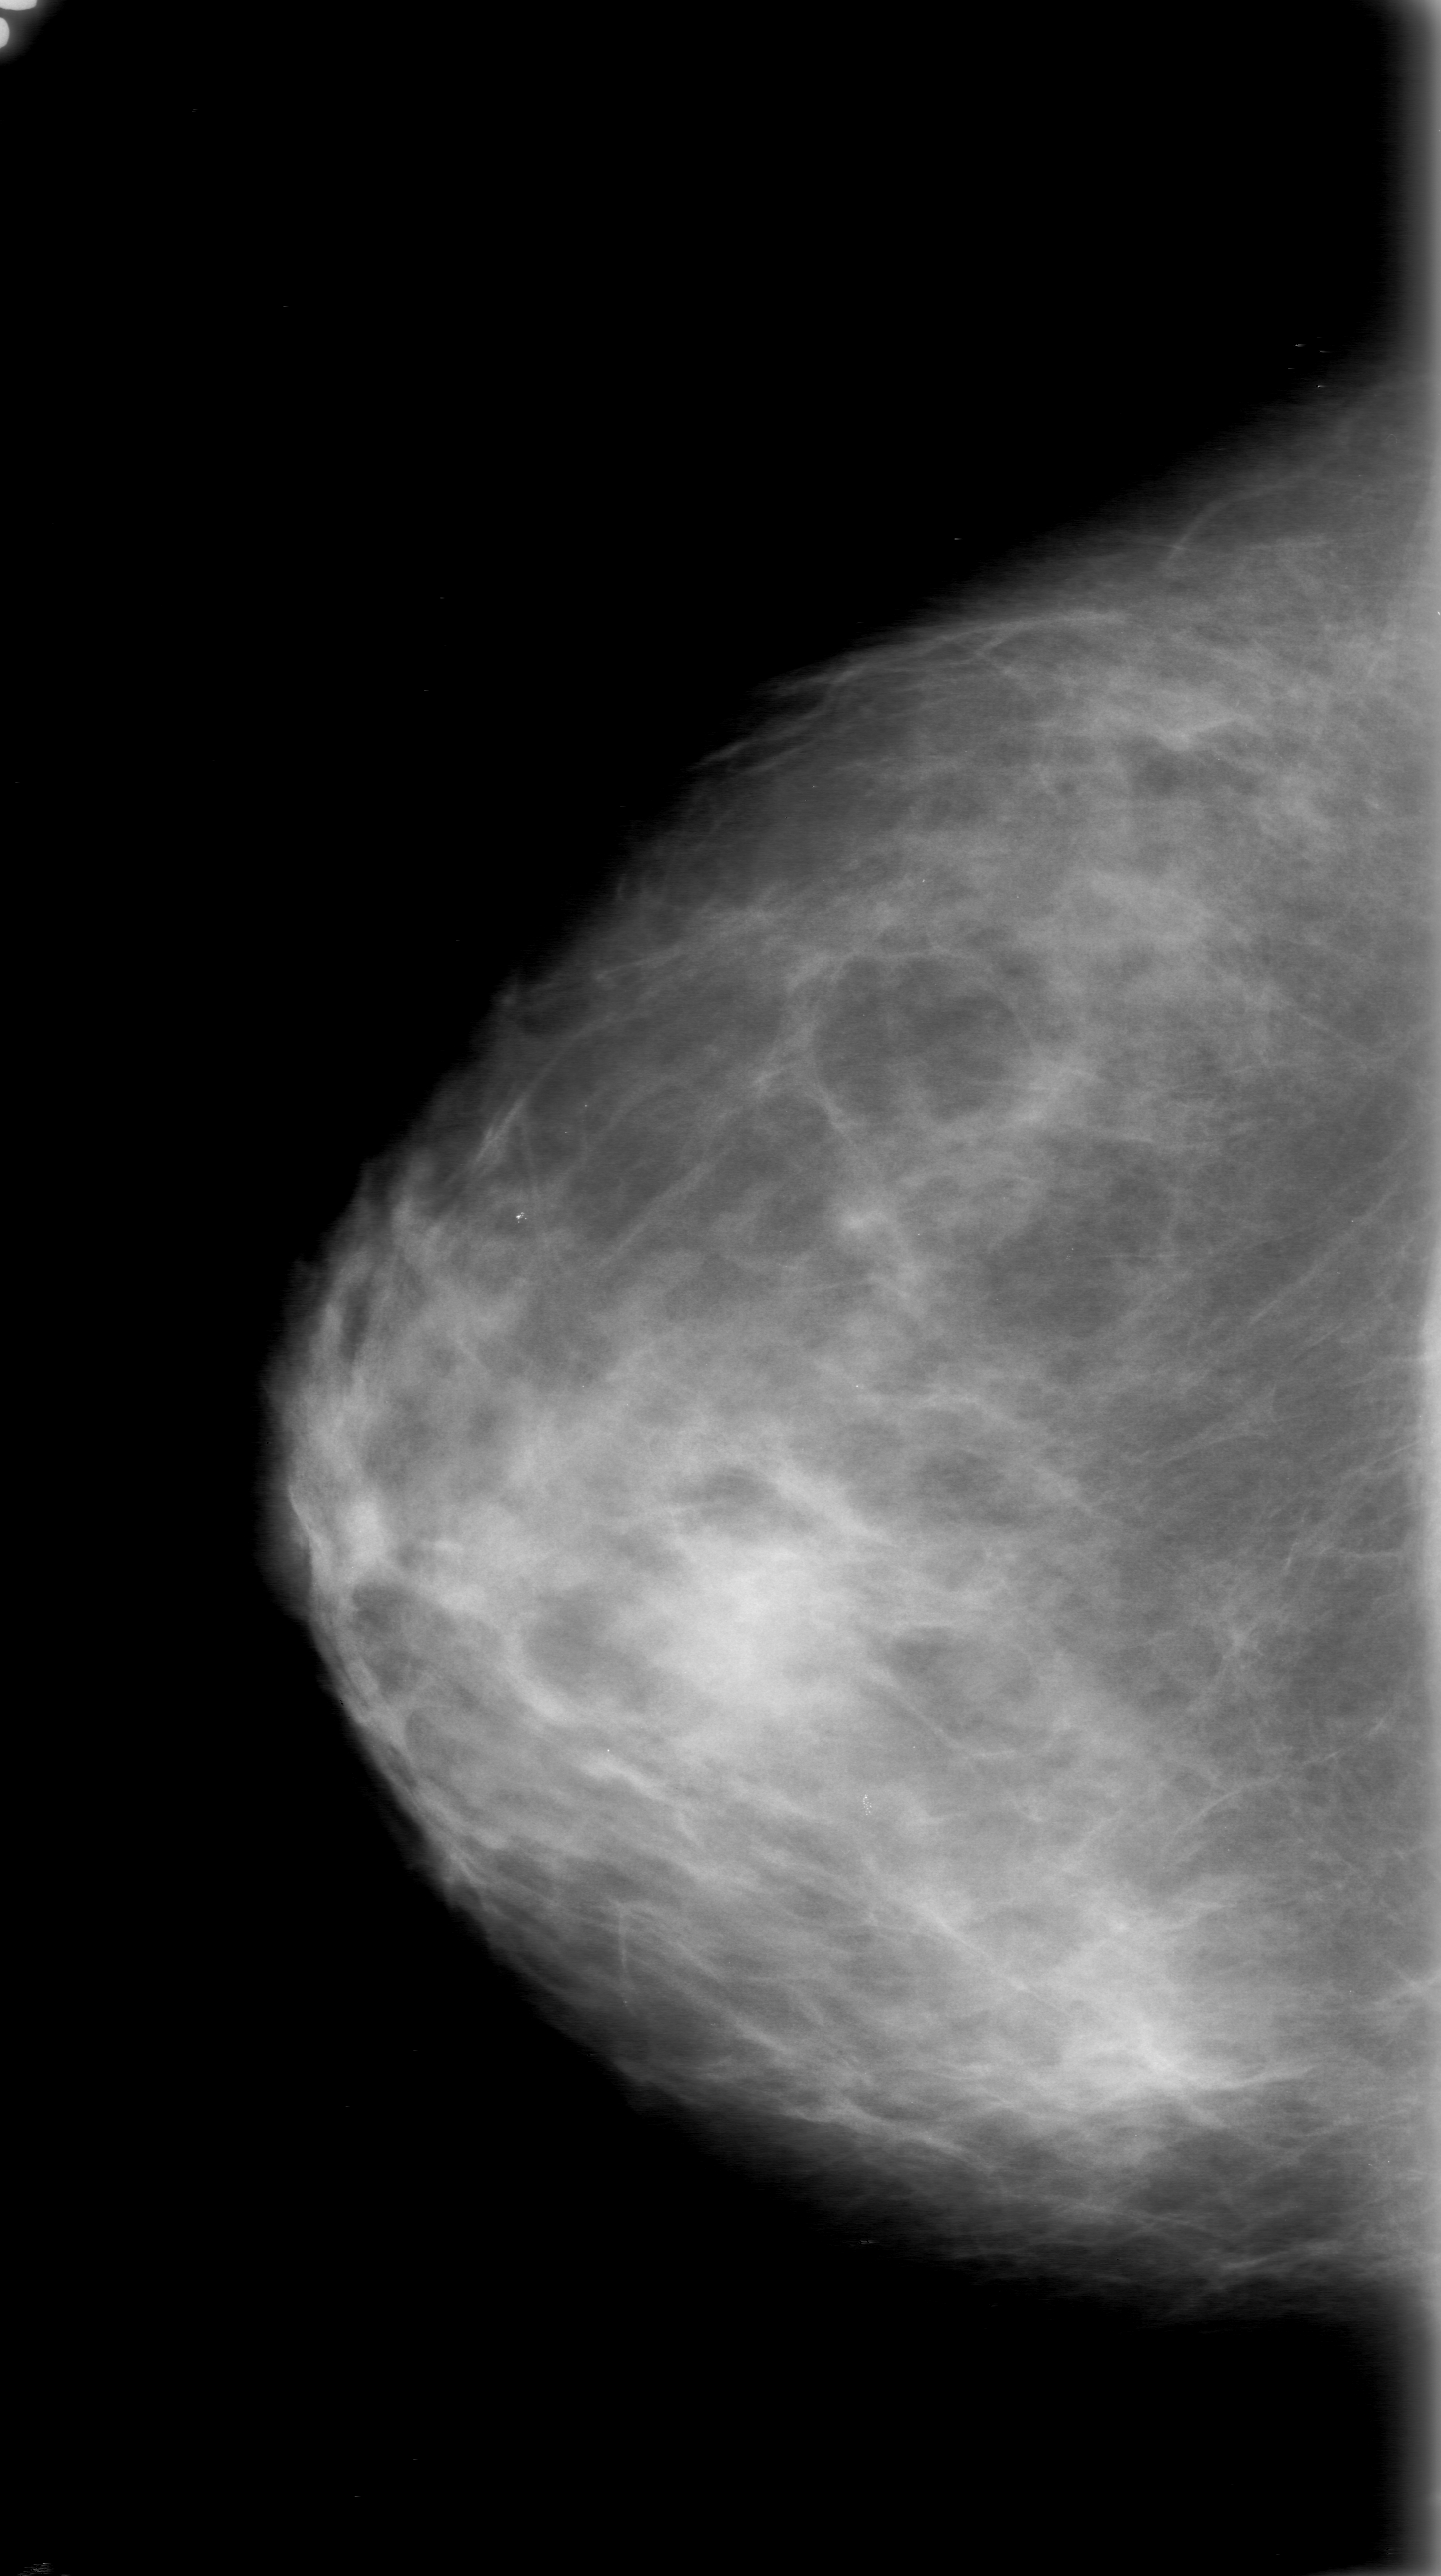
Scanned film-screen mammogram; right breast; CC view; BI-RADS breast density category 2 (scale 1–4).
- Marked abnormality: mass, shape oval, margins obscured; BI-RADS assessment category 0 (incomplete: needs additional imaging); pathology (as recorded): benign.